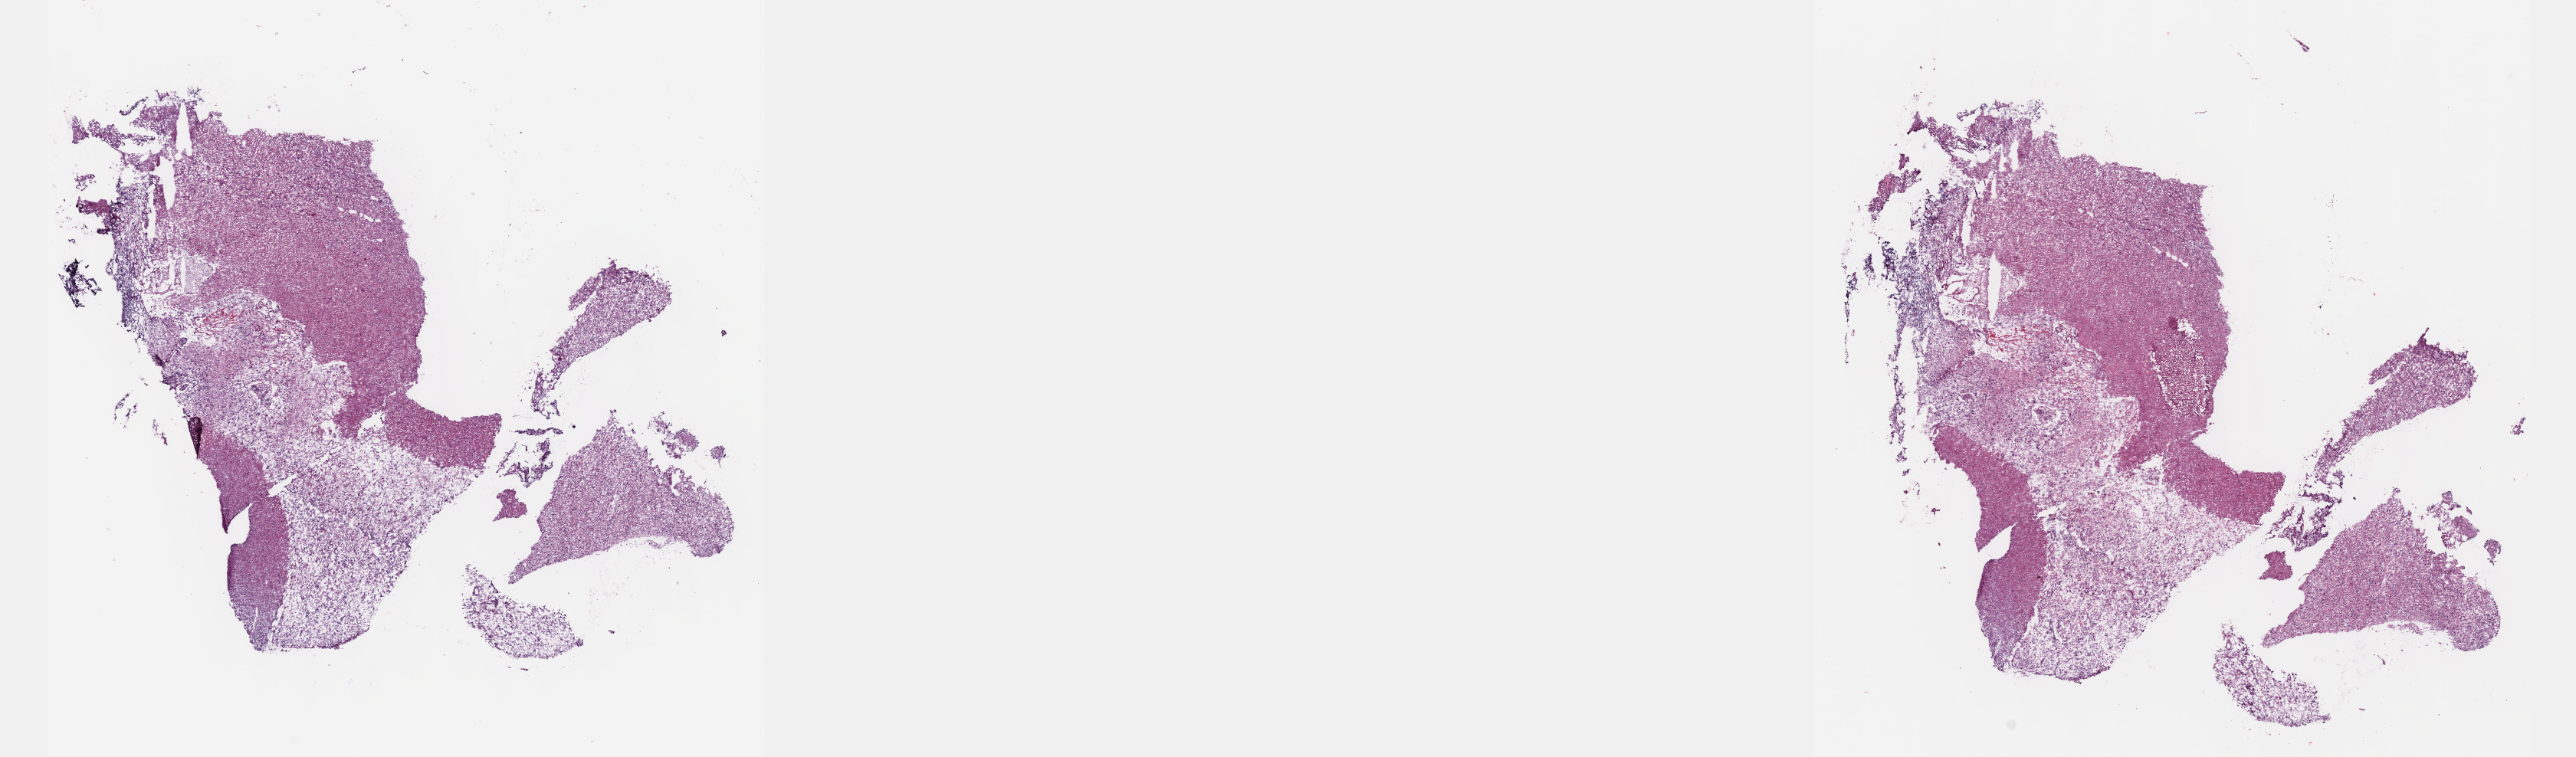
H&E-stained whole-slide image — low-resolution overview of the scanned area, about 27.2 x 8.0 mm, frozen section from the top of the tissue portion, primary tumour sample from the brain. Male, age 64 years at initial diagnosis. Composition of this section per pathologist review: tumour cells 70%, tumour nuclei 75%, normal cells 15%, stromal cells 15%, necrosis 0%. Inflammatory infiltration, as recorded: lymphocyte infiltration 0%, monocyte infiltration 0%, neutrophil infiltration 0%.
Pathologic diagnosis: Glioblastoma (frontal lobe).